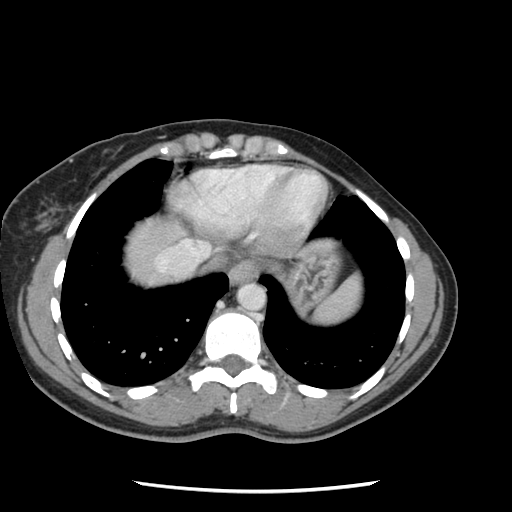
Contrast-enhanced abdominal CT, one axial slice. Slice 112 of 134 in the series (ordered by position). Intravenous contrast given. Soft-tissue window (W 400 / L 40 HU). 2.5 mm slice thickness. 512 × 512 image matrix. Female patient, age 43 years. From the clinical record (not read from this slice): diagnosis: colorectal cancer liver metastases, imaged before liver resection; multiple liver metastases: yes; largest metastasis: 3.4 cm; disease in both lobes: yes.
Structures marked on this image (outlined manually by an expert reader):
- hepatic veins: bounding box [x1, y1, x2, y2] px = [159, 240, 208, 270]
- liver: [127, 220, 179, 283]
- planned liver remnant (the part of the liver to remain after resection): [128, 220, 179, 281]